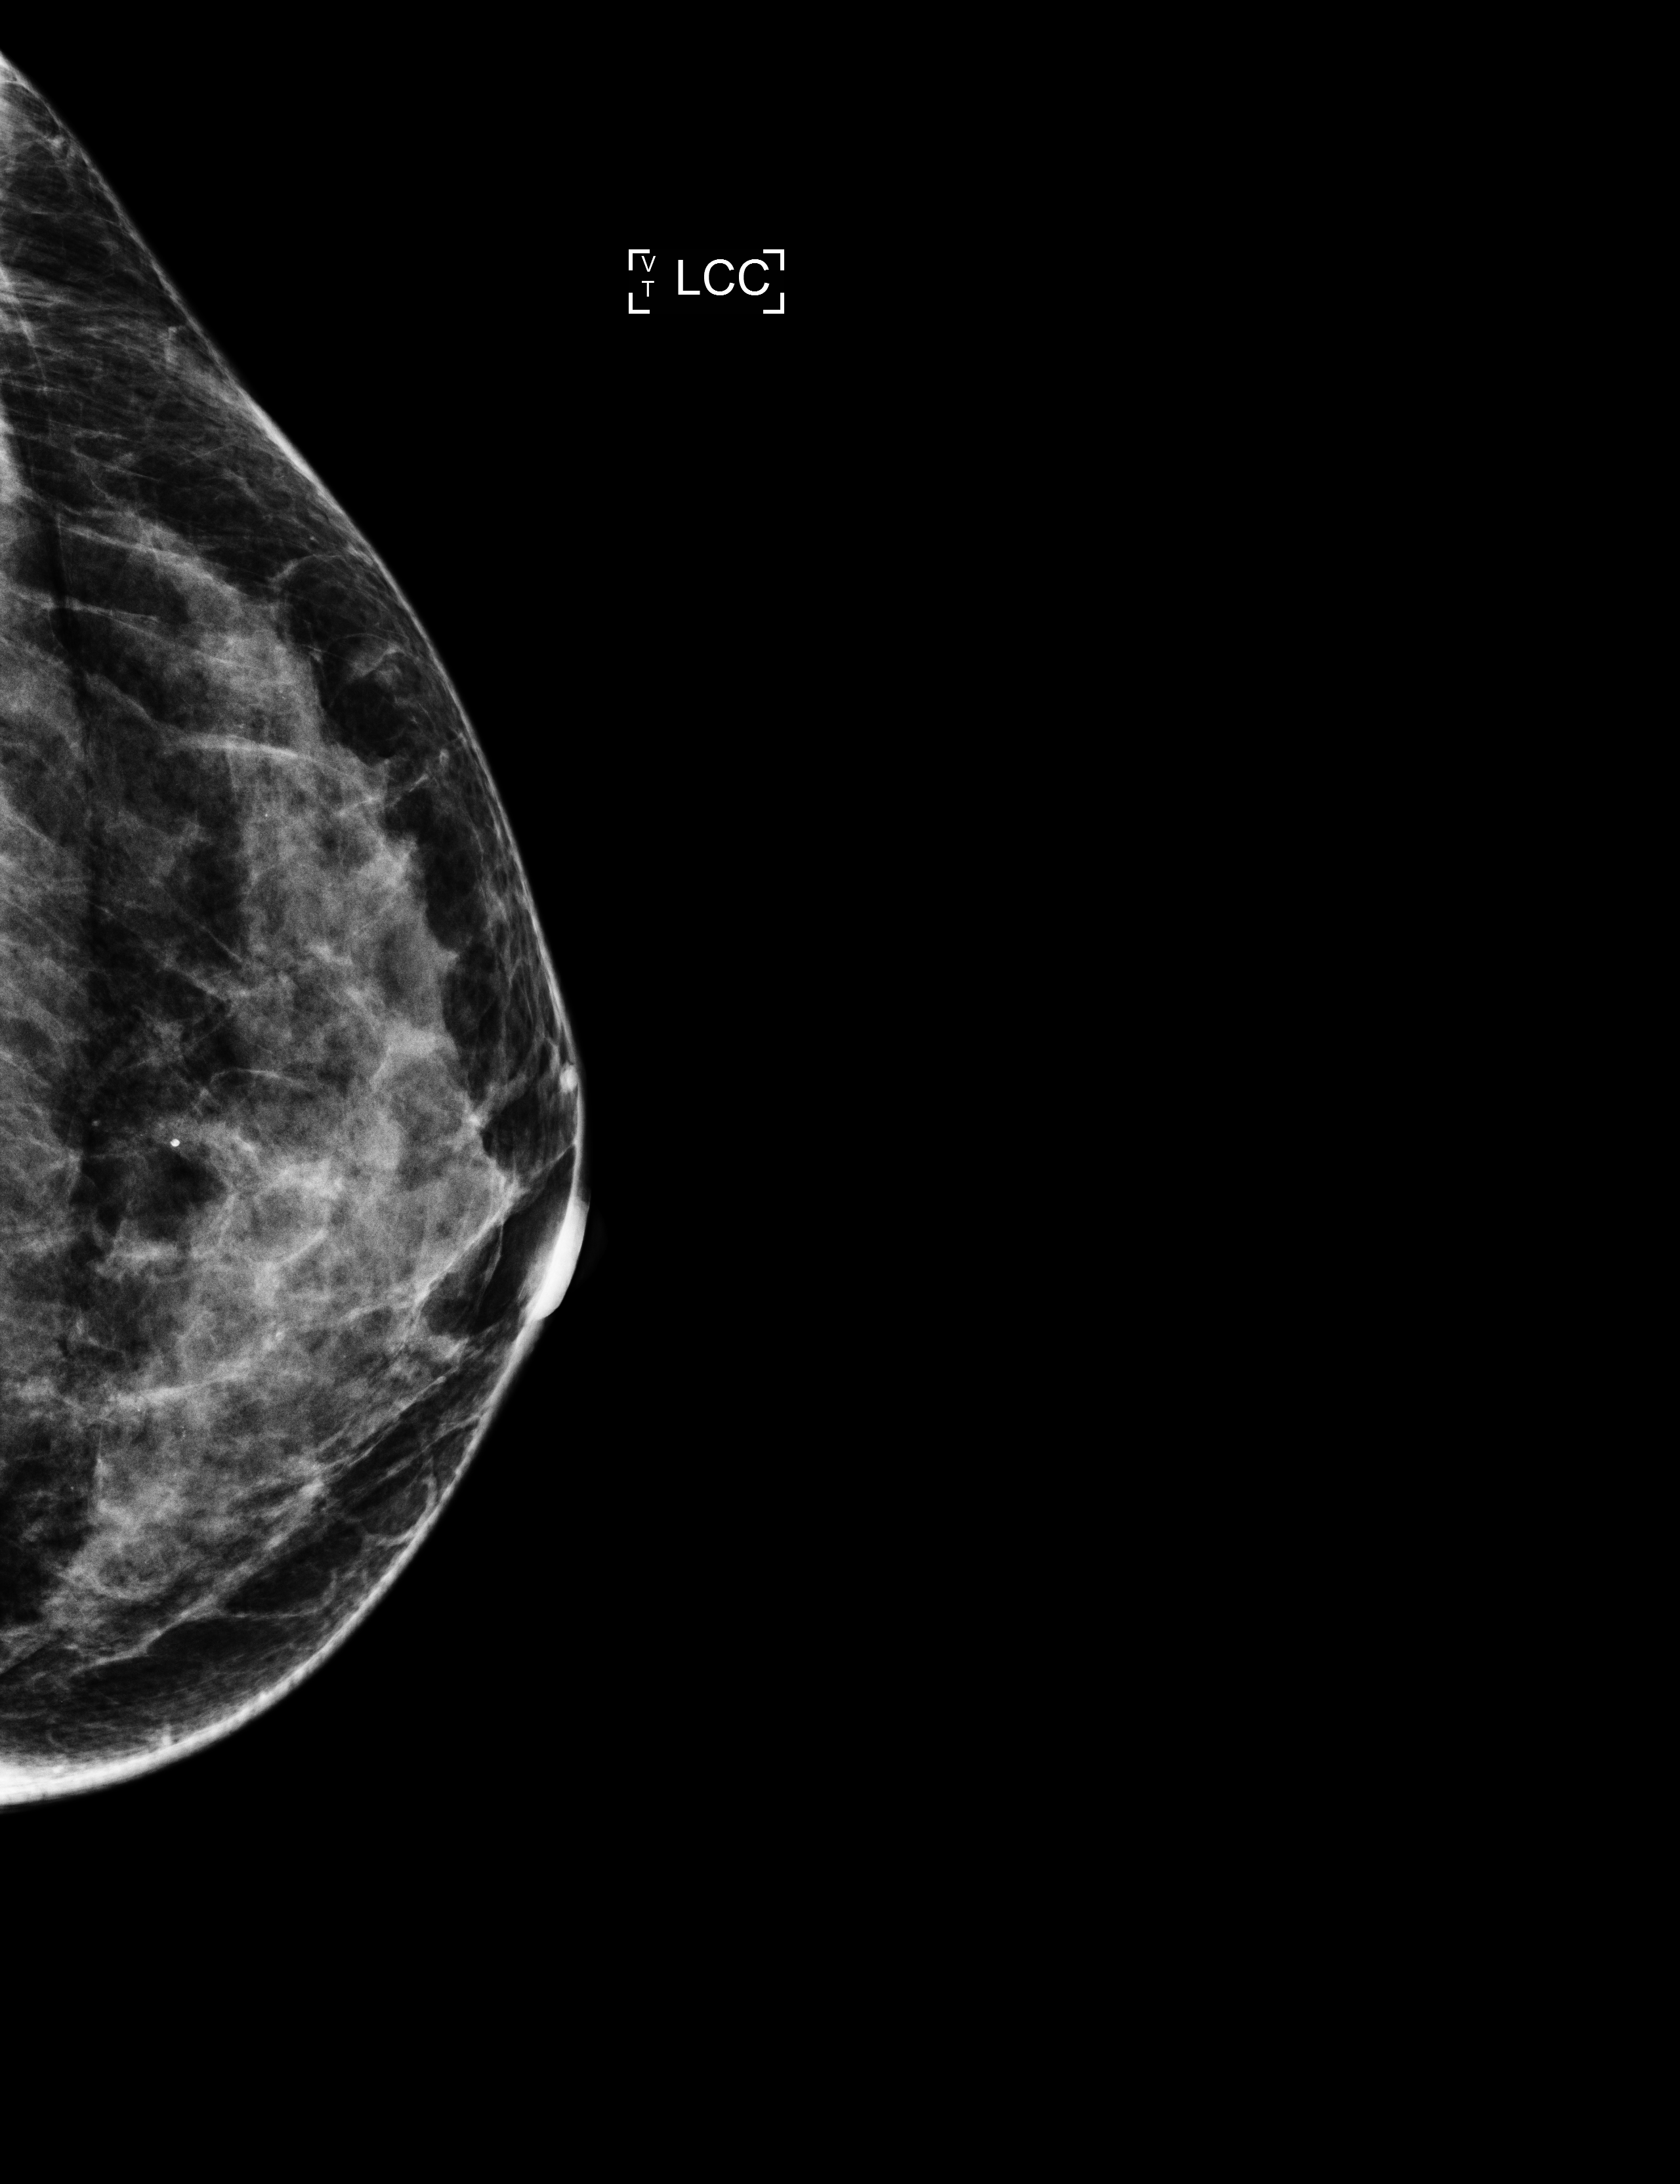
Screening examination; compressed breast thickness 40 mm; system: Selenia Dimensions. Patient aged 48 years (female).
Image type: full-field digital mammogram. Breast: left. Projection: craniocaudal (CC) view.